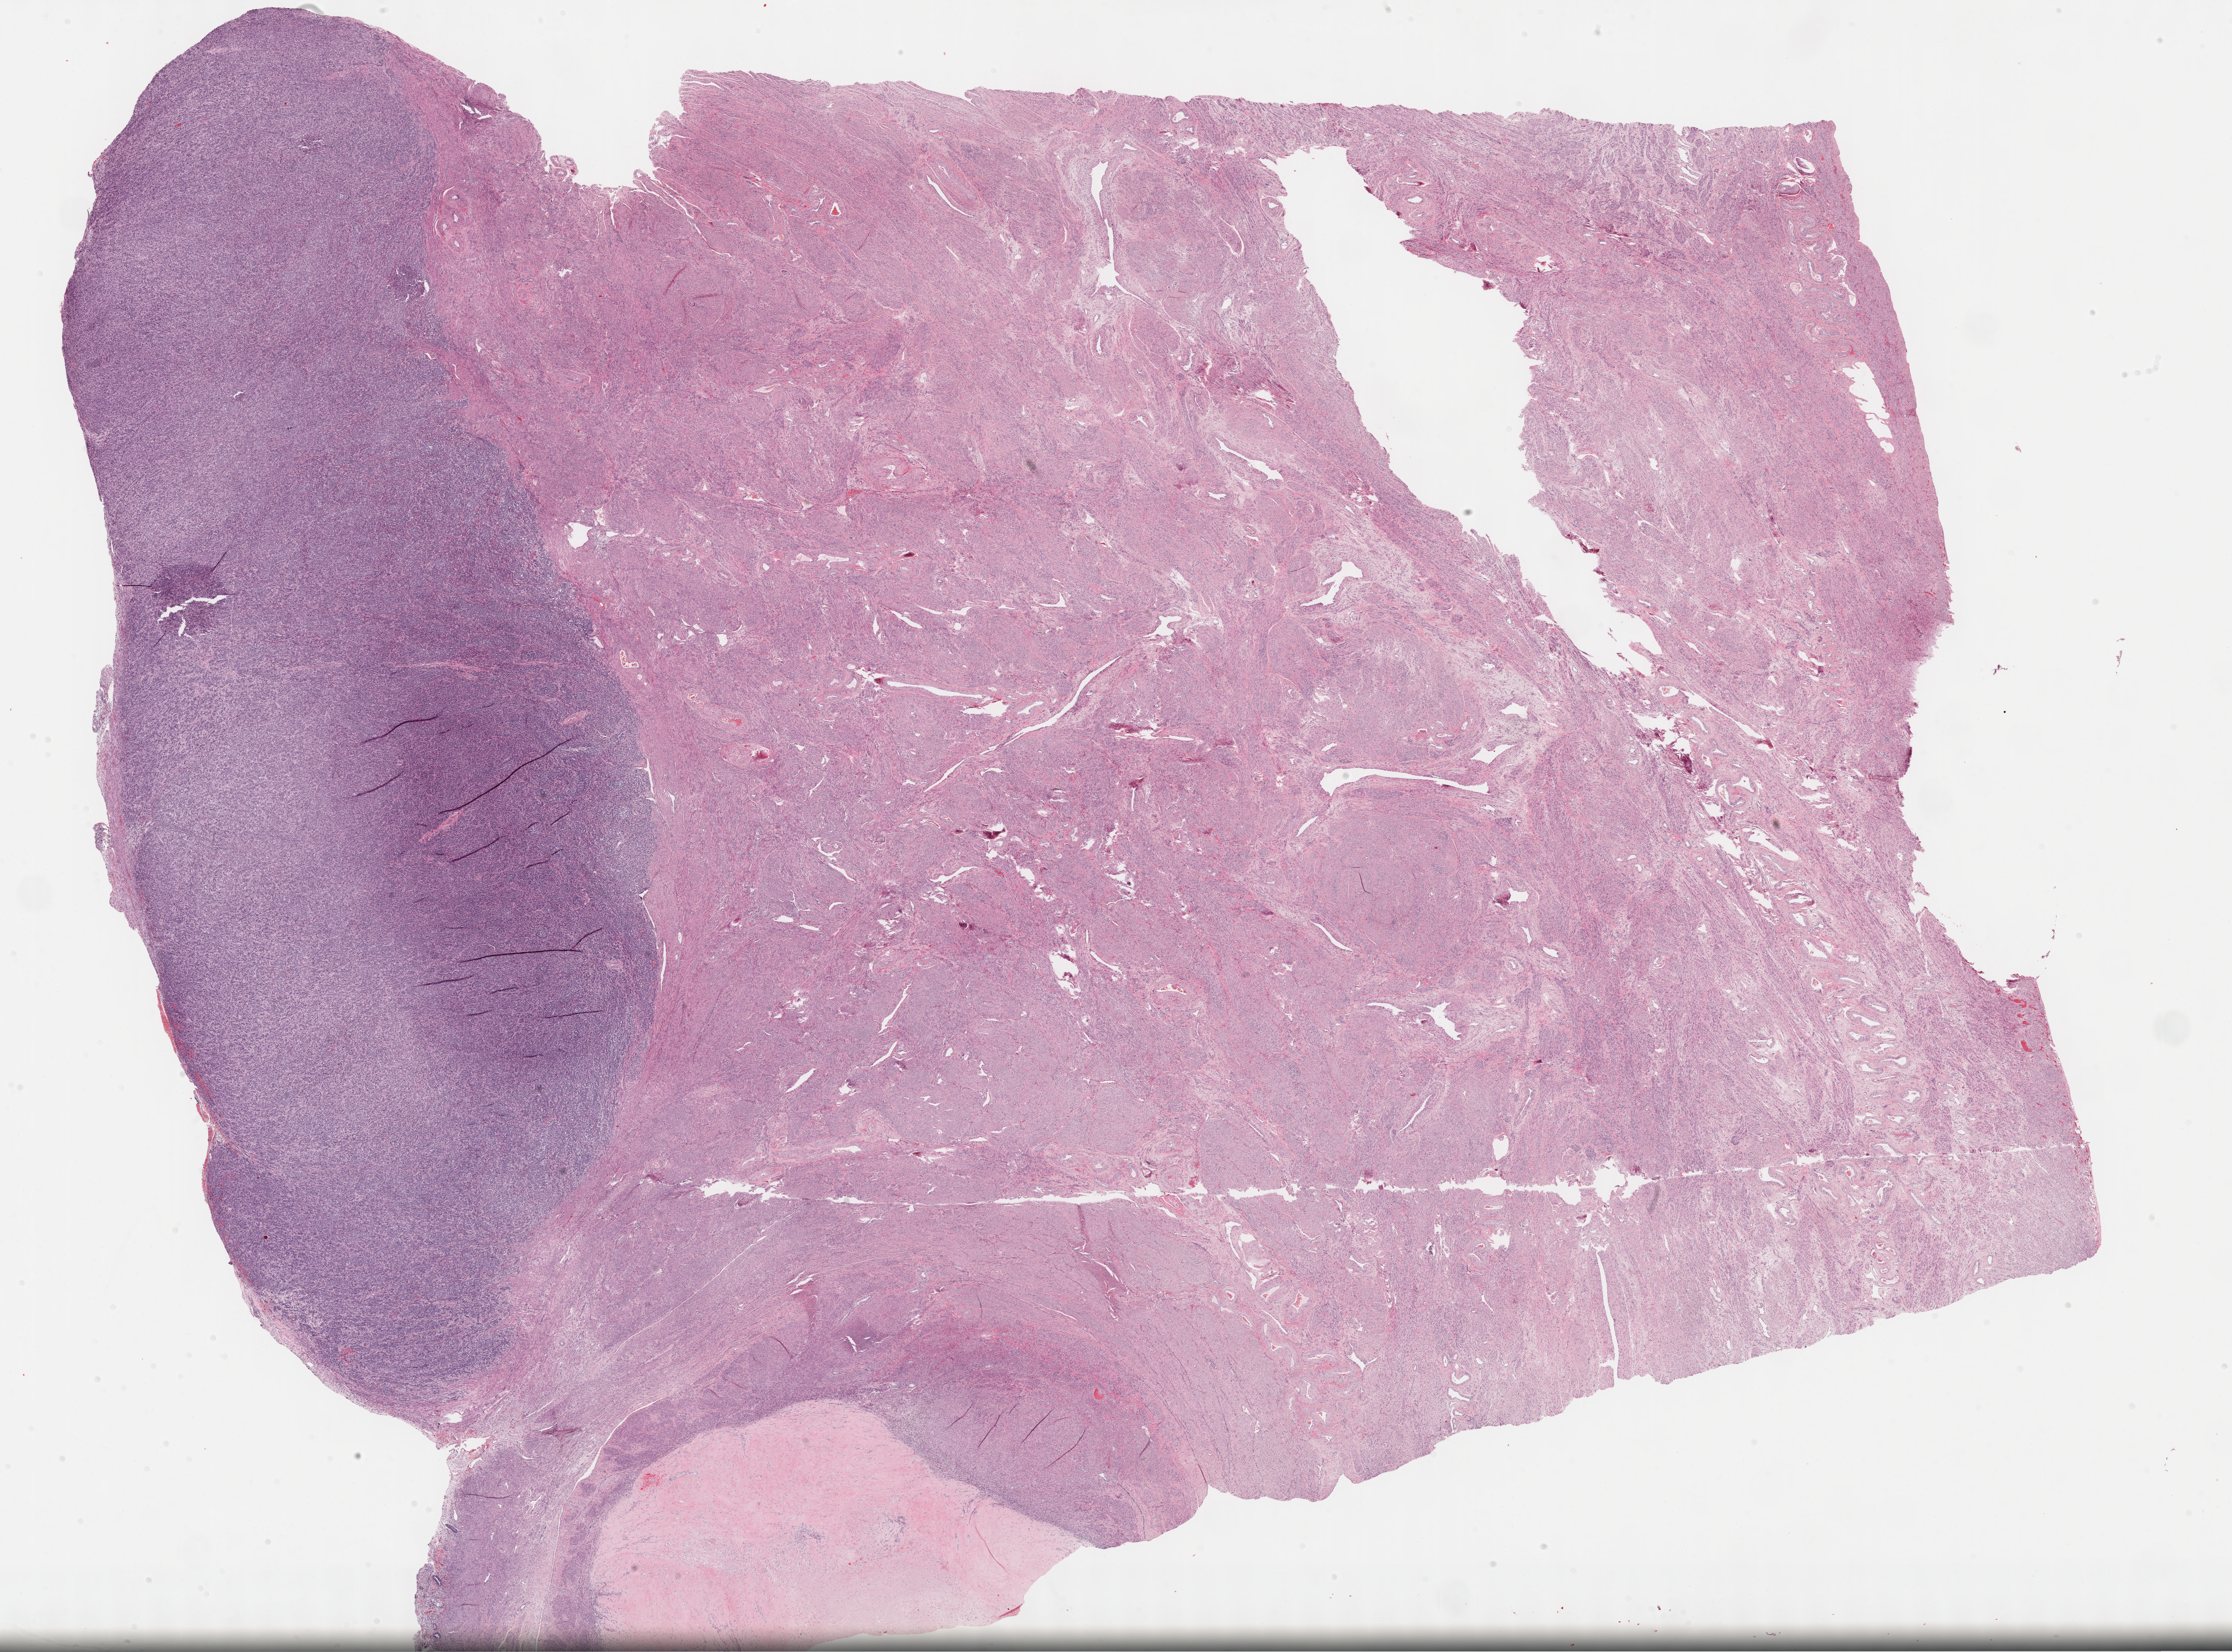
Digitized H&E-stained tissue section (whole slide), shown as a low-resolution overview of the whole scanned area (about 31.2 x 23.1 mm, acquisition: 40x scan); formalin-fixed paraffin-embedded (FFPE) diagnostic section; primary tumour sample from the skin. Female patient.
Pathologic diagnosis: Malignant melanoma, NOS.